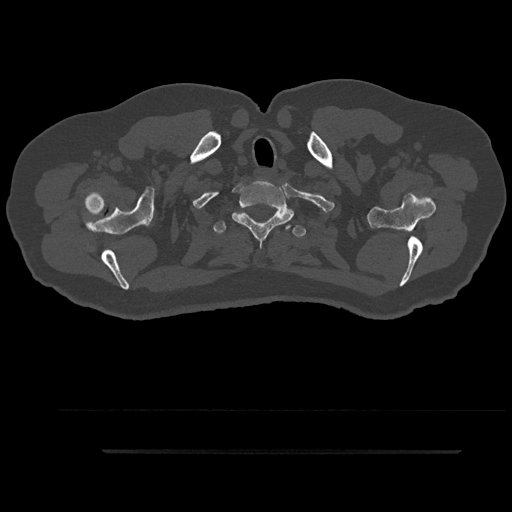
CT including the spine, one axial slice; reconstruction kernel Br40s/3; bone window (W 1800 / L 400 HU); 0.5 mm slice thickness; 512 × 512 image matrix. Patient: male, 63 years. Case-level facts recorded for this patient, not image findings: primary cancer: renal.
Annotated regions visible in this slice (semi-automatic segmentation, software-assisted and operator-edited):
- T1 vertebra: box from (x=232, y=185) to (x=296, y=246) px
- T2 vertebra: (x=213, y=221)–(x=306, y=238)